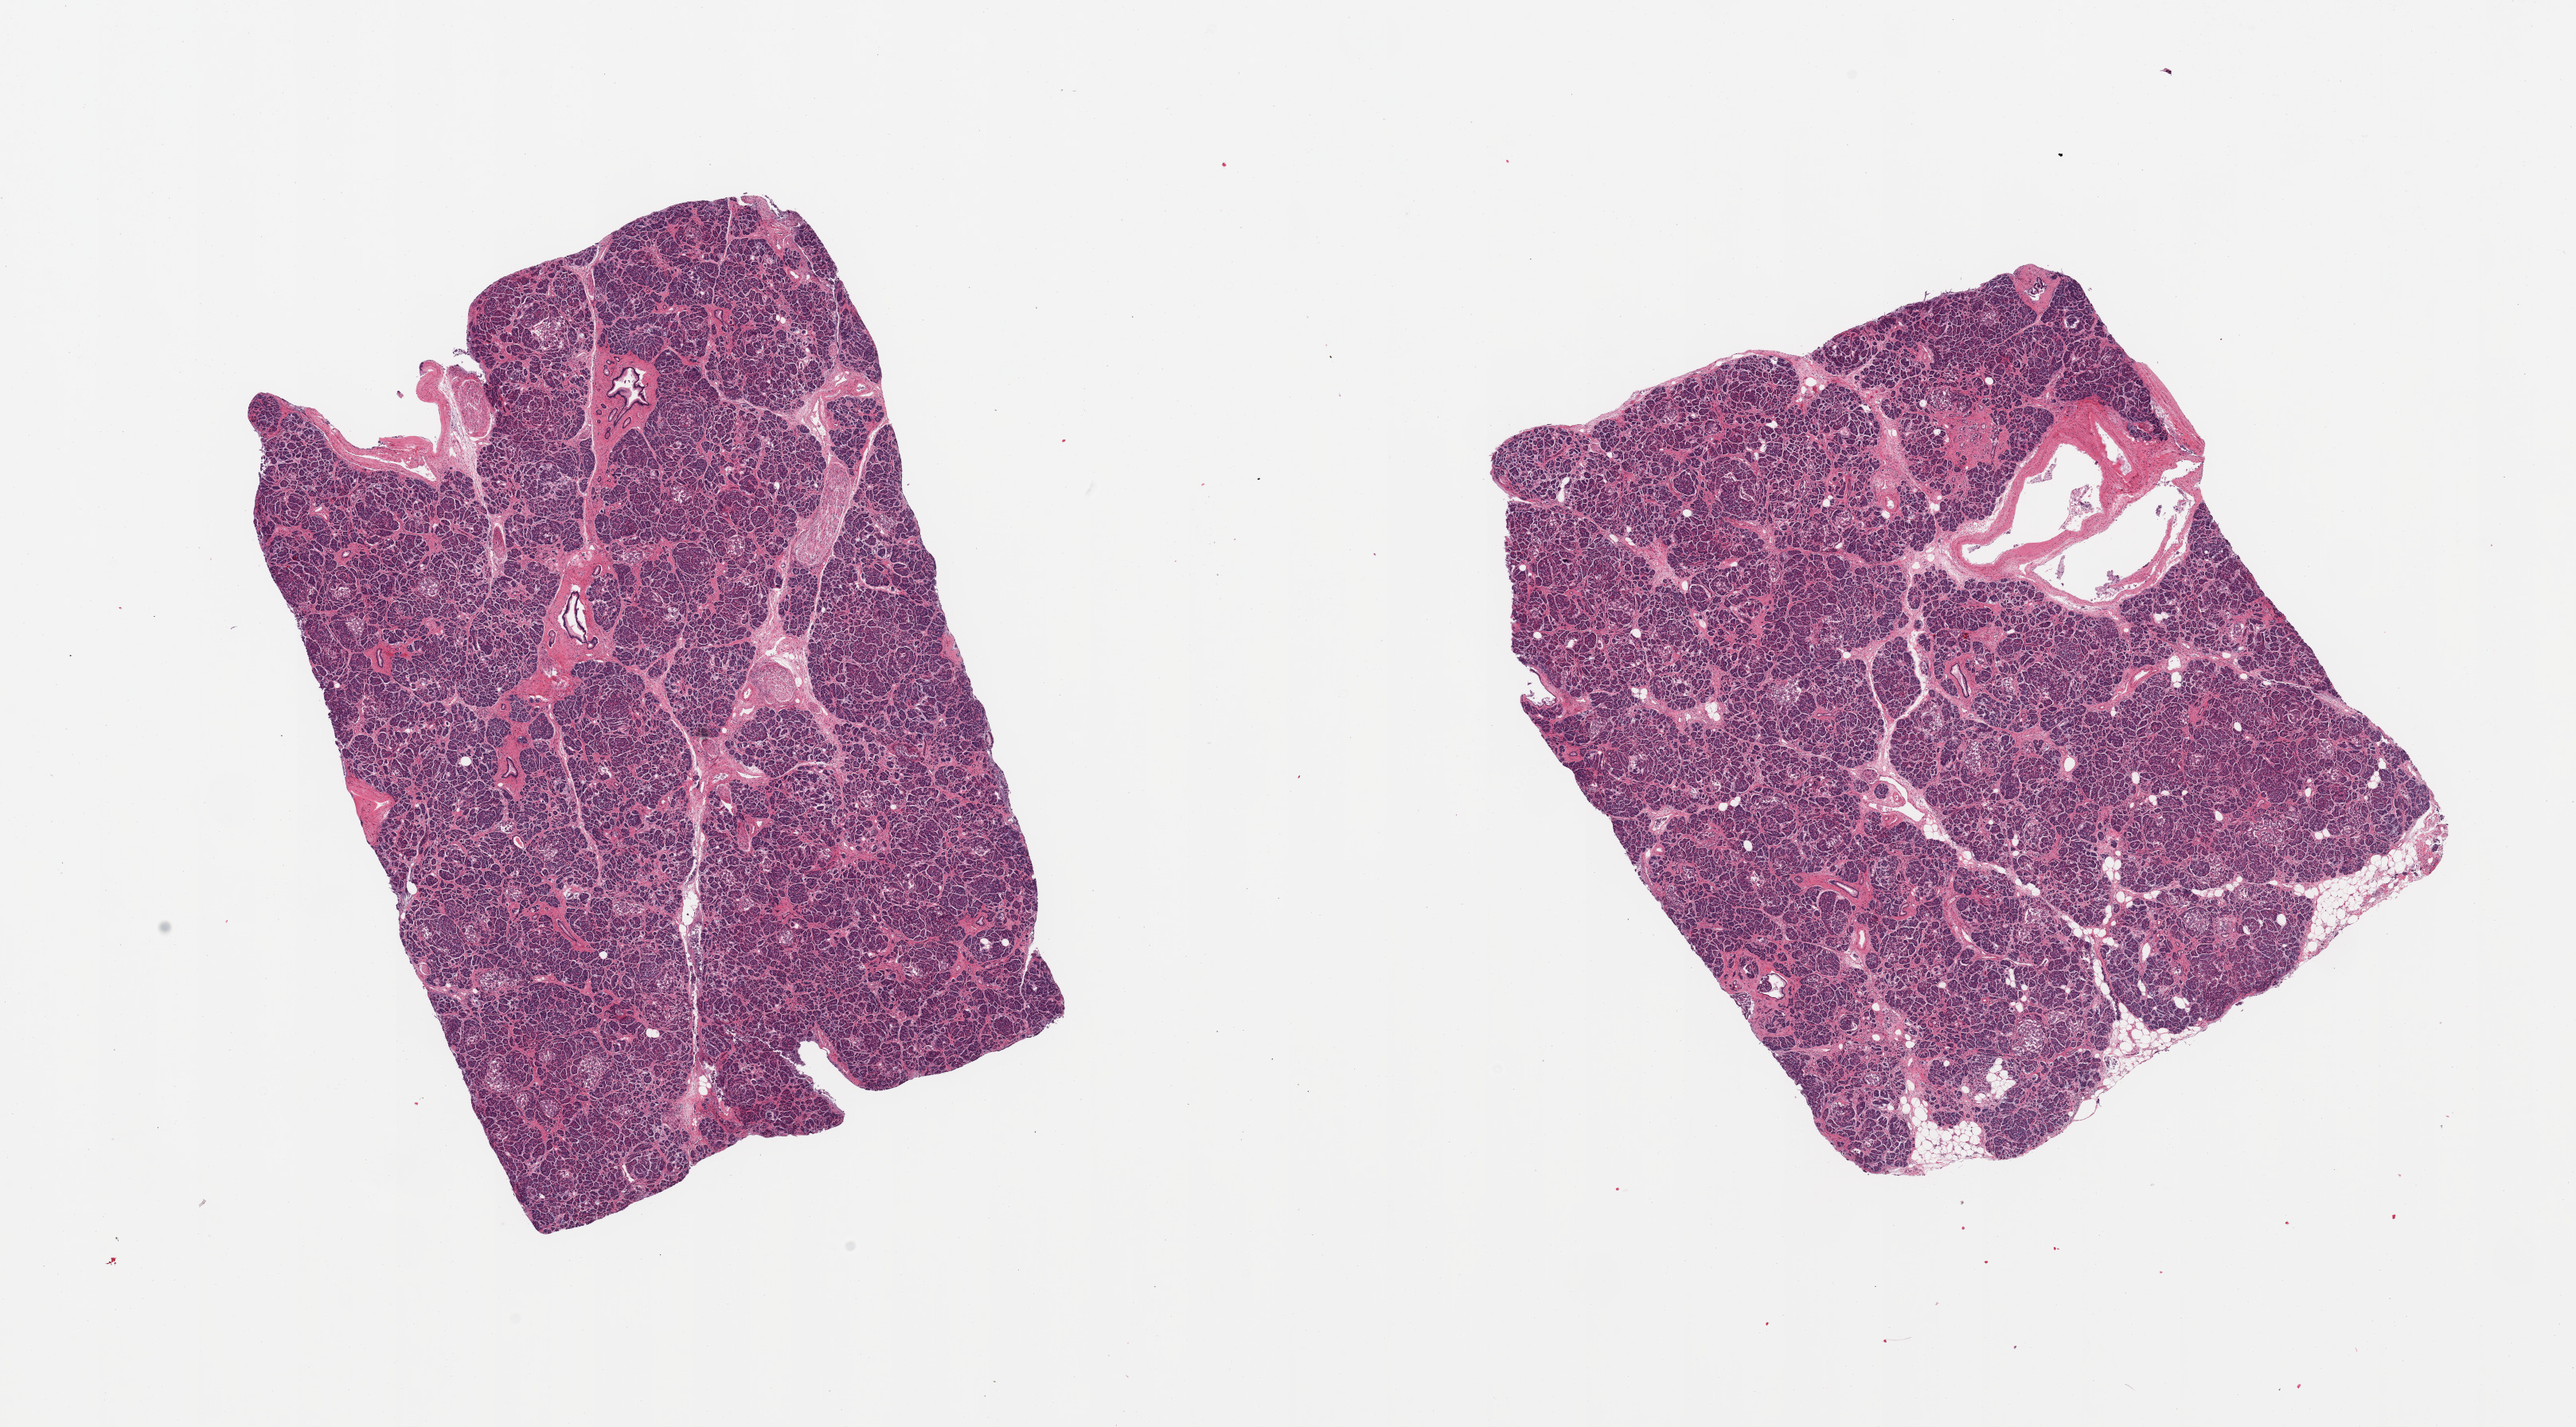
Digitized haematoxylin and eosin-stained section, brightfield — whole scanned area (about 25.6 x 14.2 mm, acquisition: 20x scan) shown as a low-resolution overview. PAXgene-fixed paraffin-embedded (PFPE) section. Section of pancreas (target tissue). Tissue donor sample.
- review note (as recorded): 2 pieces; mild to moderate diffuse fibrosis; 5% external fat on 1 piece